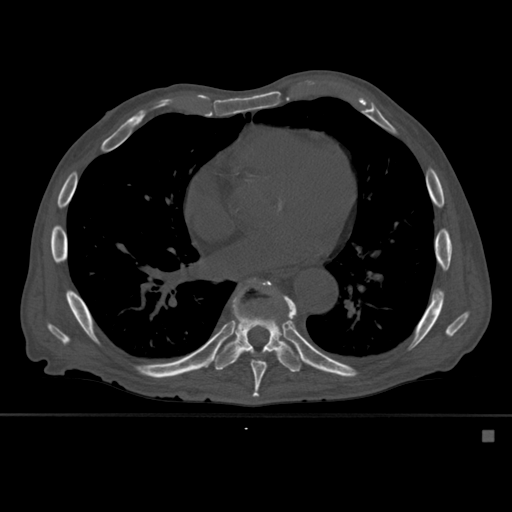
CT including the spine, one axial slice. Slice 341 of 527 in the series (ordered by position). Bone window (W 1800 / L 400 HU). 1.5 mm slice thickness. 512 × 512 image matrix. Male patient, age 78 years. From the clinical record (not read from this slice): primary cancer: prostate.
Outlined on this slice (semi-automatically segmented with operator editing):
- T8 vertebra: bounding box (x1, y1, x2, y2) in pixels: (247, 279, 288, 398)
- T9 vertebra: (213, 282, 305, 373)